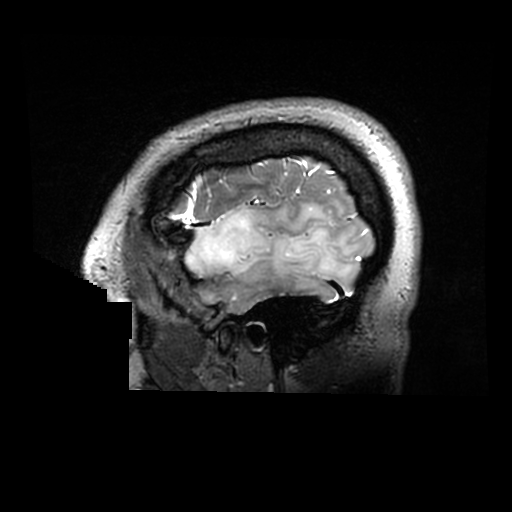
Brain MRI from a brain-tumour surgery series, one sagittal slice; position 246 of 320 along the scan axis; 0.6 mm slice thickness; 512 × 512 image matrix. From the clinical record (not read from this slice): histopathology: Astrocytoma; WHO grade: 2; IDH mutation: yes.
Structures marked on this image (expert manual segmentation):
- tumour: bounding box [x1, y1, x2, y2] px = [185, 201, 353, 288]